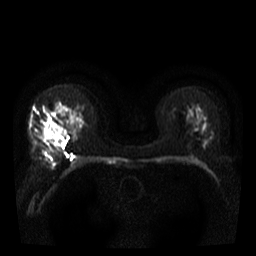
Breast MRI, one axial slice; position 21 of 40 along the scan axis; diffusion-weighted series; image 2 of 4 stored at this slice position (different b-values; order by instance number); 3 T; 5 mm slice thickness; 256 × 256 image matrix, field of view 300 × 300 mm. Female patient.
Structures marked on this image (outlined manually by an expert reader):
- tumour on diffusion-weighted imaging: bounding box <47,130,63,145> (left, top, right, bottom; pixels)